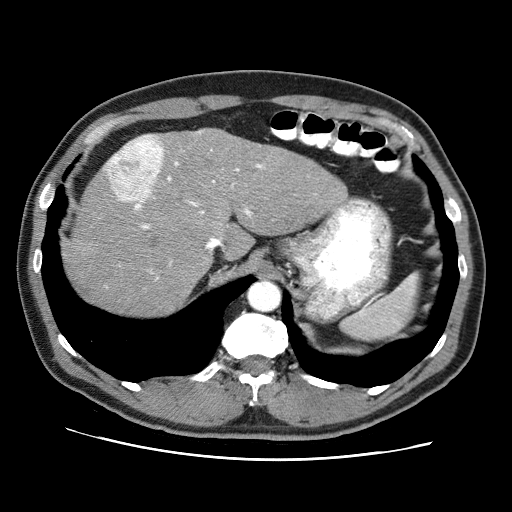
Contrast-enhanced abdominal CT (liver protocol), one axial slice; position 54 of 71 along the scan axis; reconstruction kernel STANDARD; soft-tissue window (W 400 / L 40 HU); 512 × 512 image matrix, field of view 360 × 360 mm. From the clinical record (not read from this slice): diagnosis: hepatocellular carcinoma (patient treated with transarterial chemoembolisation; whether this scan precedes or follows treatment is not stated here); TNM stage (as recorded): Stage-II; Child-Pugh class: A; tumour differentiation: well differentiated.
Structures marked on this image (semi-automatically segmented with operator editing):
- abdominal aorta: box from (x=249, y=282) to (x=279, y=310) px
- liver parenchyma outside the tumour (the mass and vessels are separate outlines, so this box may not span the whole liver): (x=64, y=128)–(x=346, y=316)
- mass: (x=103, y=134)–(x=163, y=202)
- liver vessels: (x=135, y=162)–(x=262, y=279)